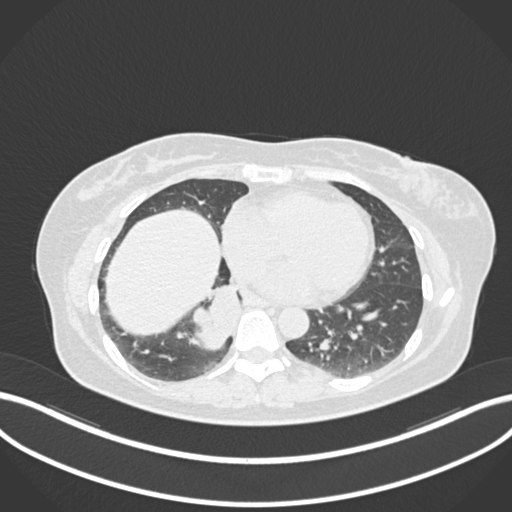
Chest CT, one axial slice; slice 553 of 677 in the series (ordered by position); reconstruction kernel B30f; lung window (W 1500 / L -600 HU); 1 mm slice thickness; 512 × 512 image matrix. Patient: female, 54 years. From the clinical record (not read from this slice): clinical TNM (as recorded): T4 N0 M0.
Annotated regions visible in this slice (bounding box drawn by a radiologist):
- lung tumour (recorded histology: adenocarcinoma): bounding box <182,273,242,357> (left, top, right, bottom; pixels)